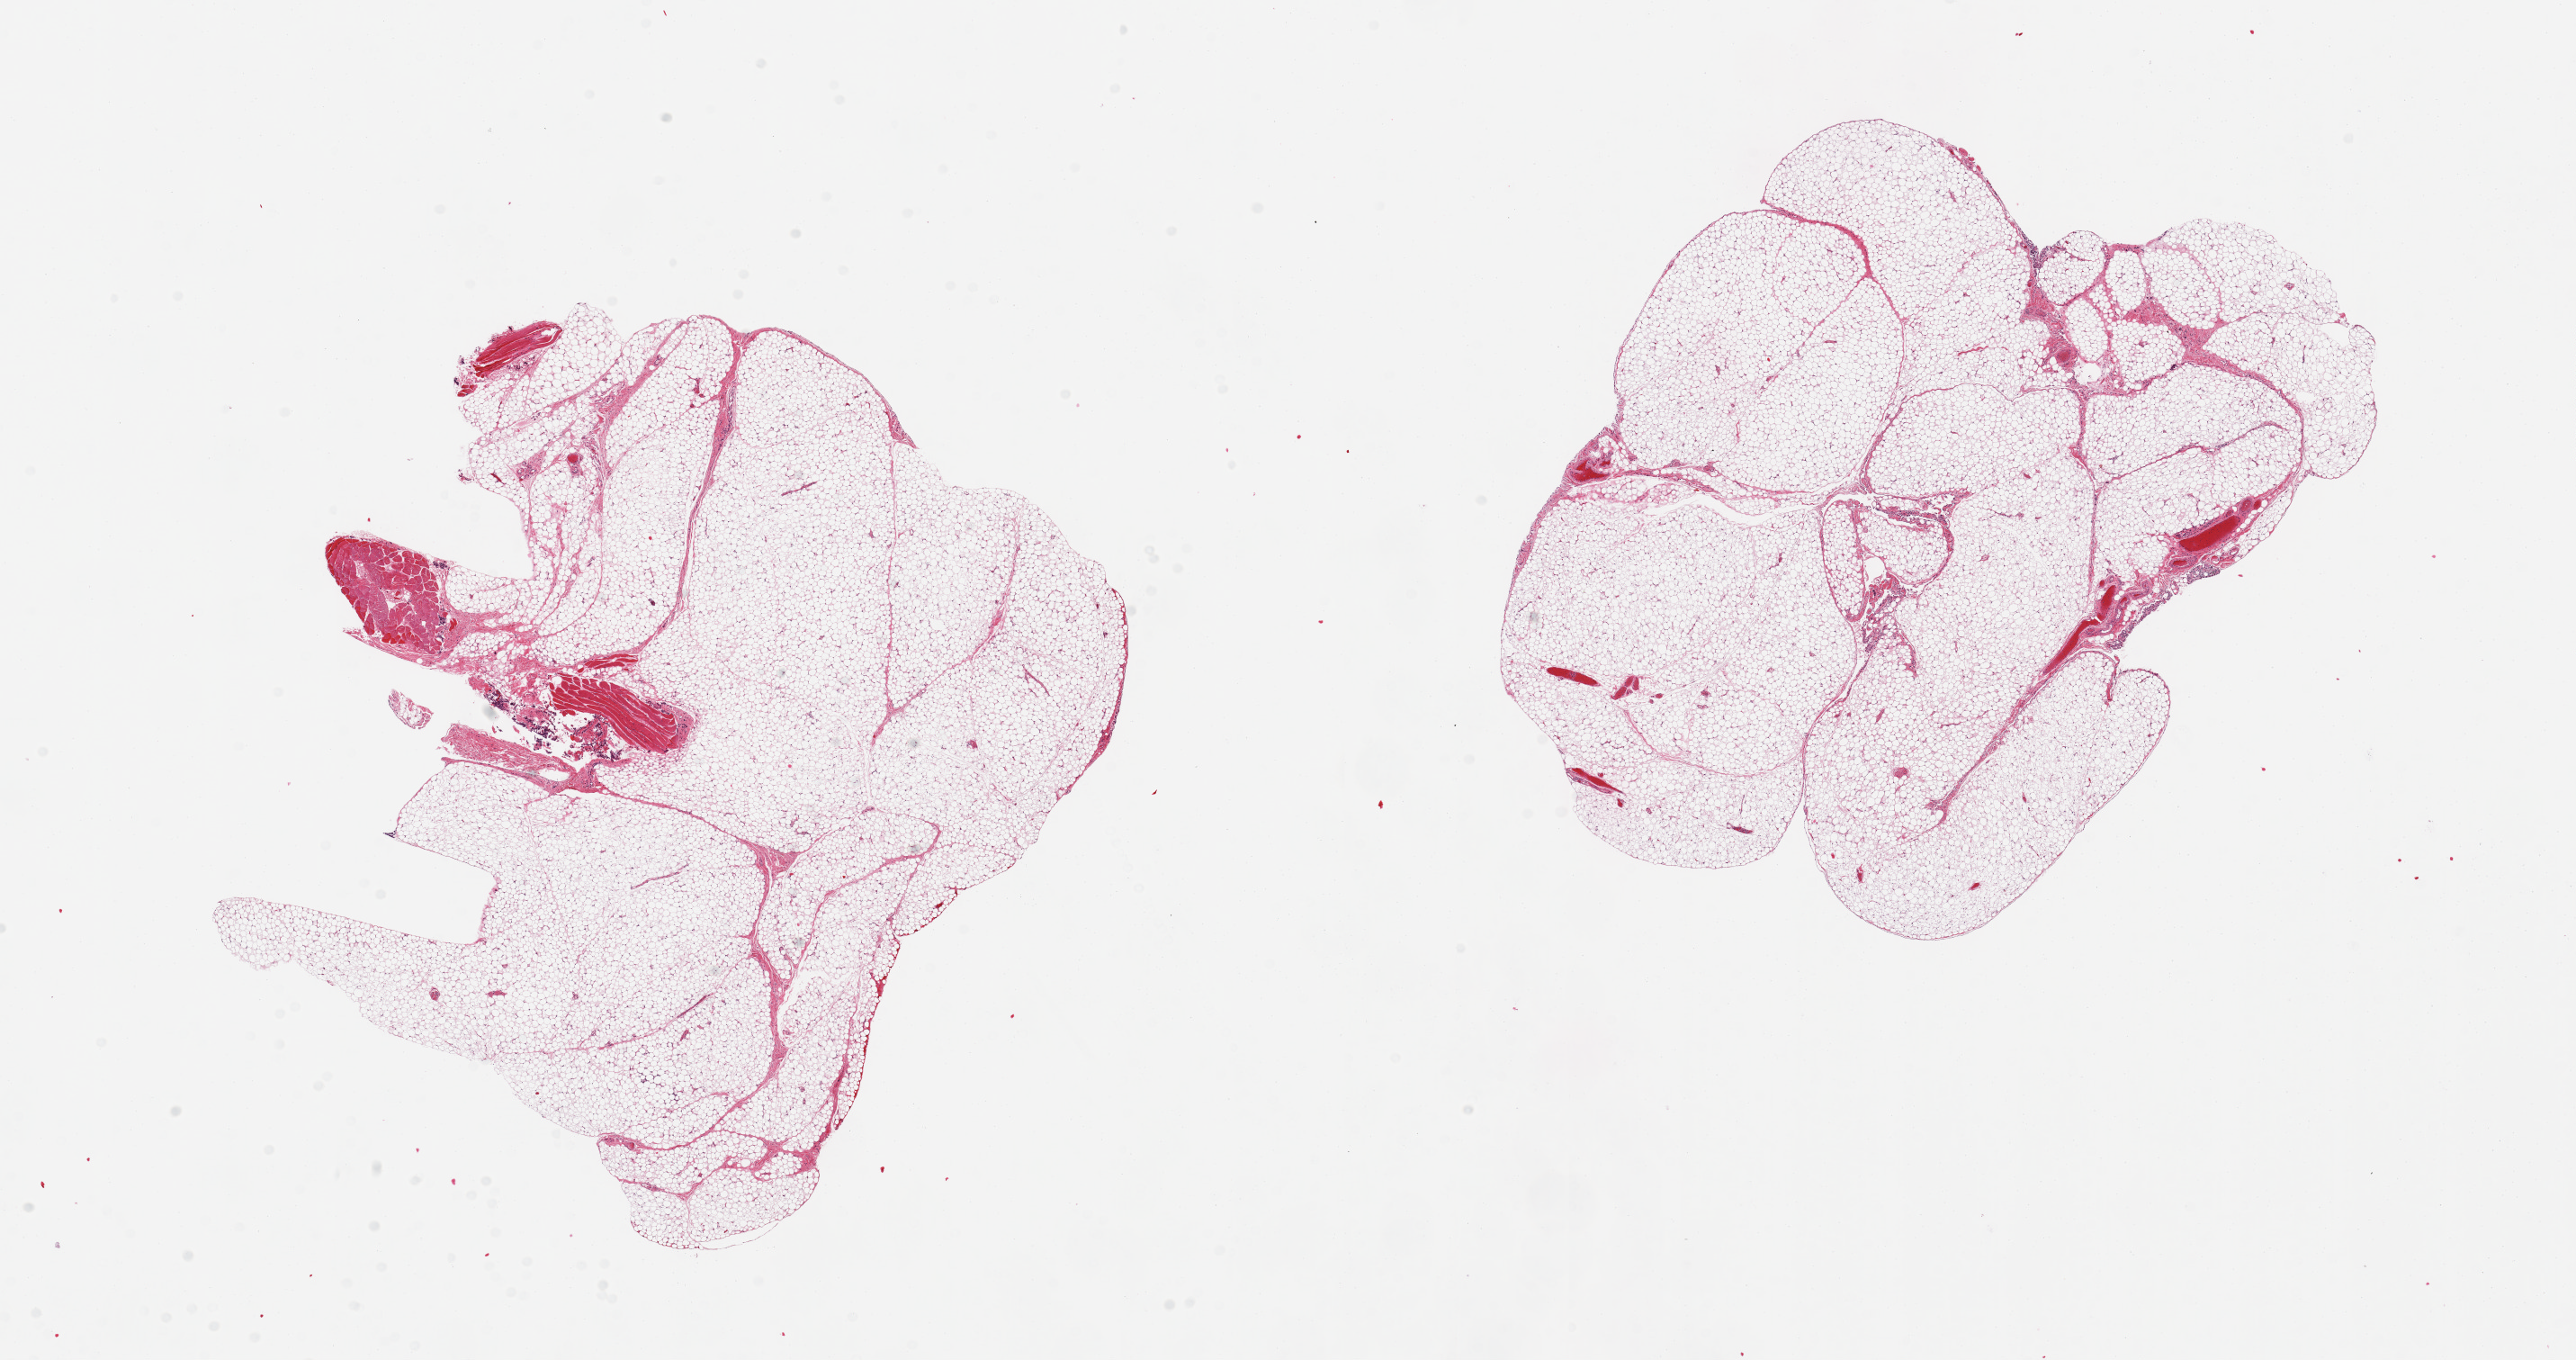
Whole-slide image, hematoxylin and eosin (H&E) stain, brightfield, low-resolution overview of the scanned area, about 22.6 x 11.9 mm. PAXgene-fixed, paraffin-embedded tissue. Section of omentum (target tissue). Donor tissue sample.
• pathologist's review note for this sample: 2 pieces; fascia/vascular elements/adherent muscle (skeletal) are ~10-15% of tissue